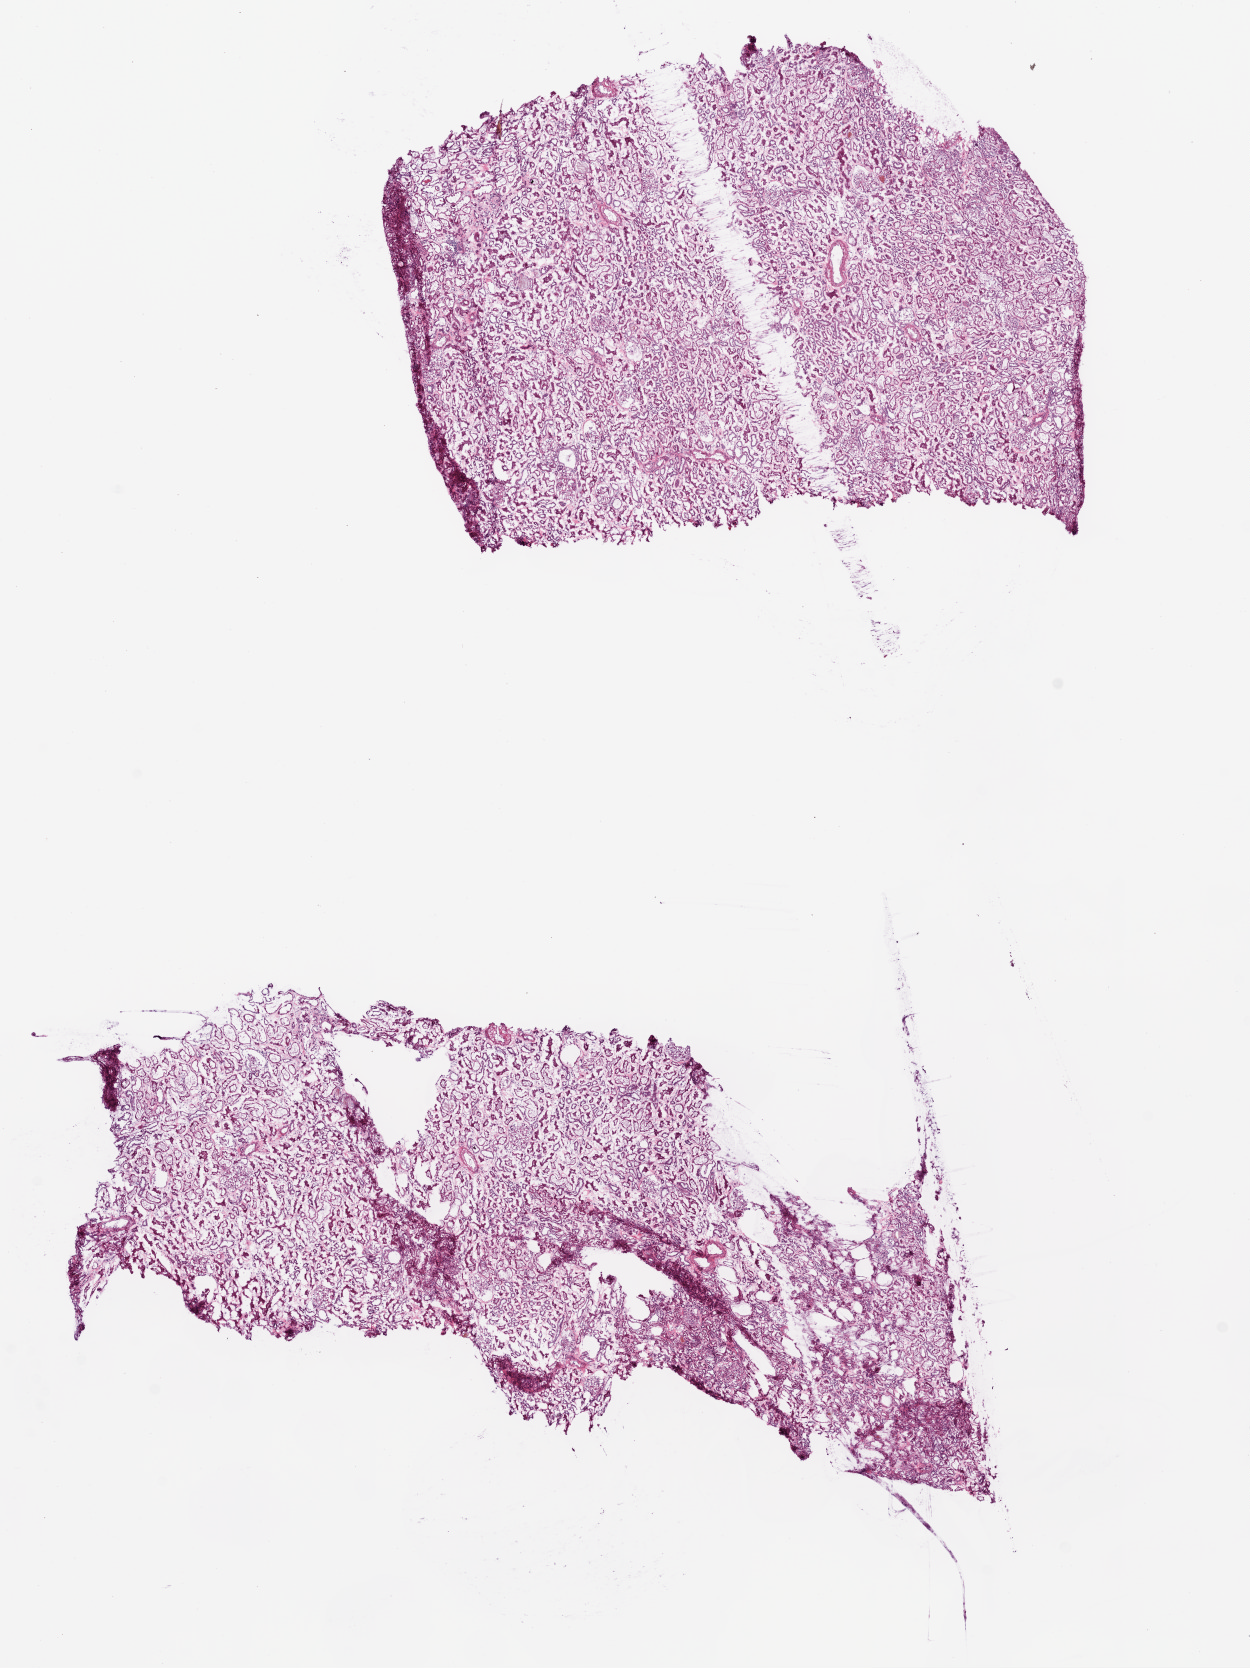
Whole-slide histology image, H&E-stained, shown as a low-resolution overview of the whole scanned area (about 10.0 x 13.4 mm, acquisition: 20x scan), frozen section, sample: solid tissue normal (non-tumour tissue), kidney. Male patient; age at initial diagnosis 60 years.
This section: solid tissue normal sample (biorepository sample class). Patient diagnosis: Clear cell adenocarcinoma, NOS.